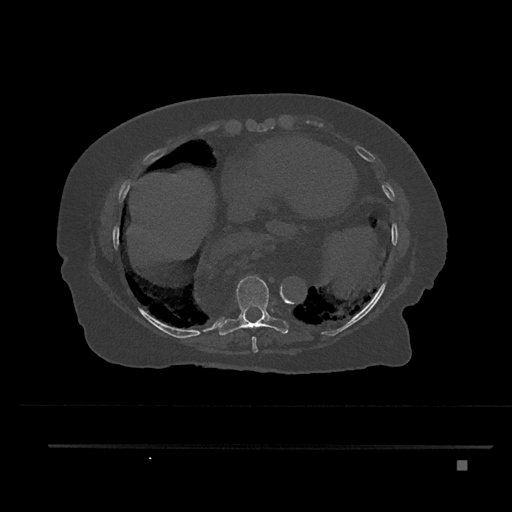
CT including the spine, one axial slice. Position 406 of 797 along the scan axis. 120 kVp. Bone window (W 1800 / L 400 HU). 512 × 512 image matrix, field of view 437 × 437 mm. Patient: female, 76 years. Case-level facts recorded for this patient, not image findings: primary cancer: lung; vertebrae with lytic lesions (as recorded): T11, L3.
Annotated regions visible in this slice (semi-automatic segmentation, software-assisted and operator-edited):
- T8 vertebra: bounding box (x1, y1, x2, y2) in pixels: (252, 336, 258, 353)
- T9 vertebra: (217, 276, 289, 336)